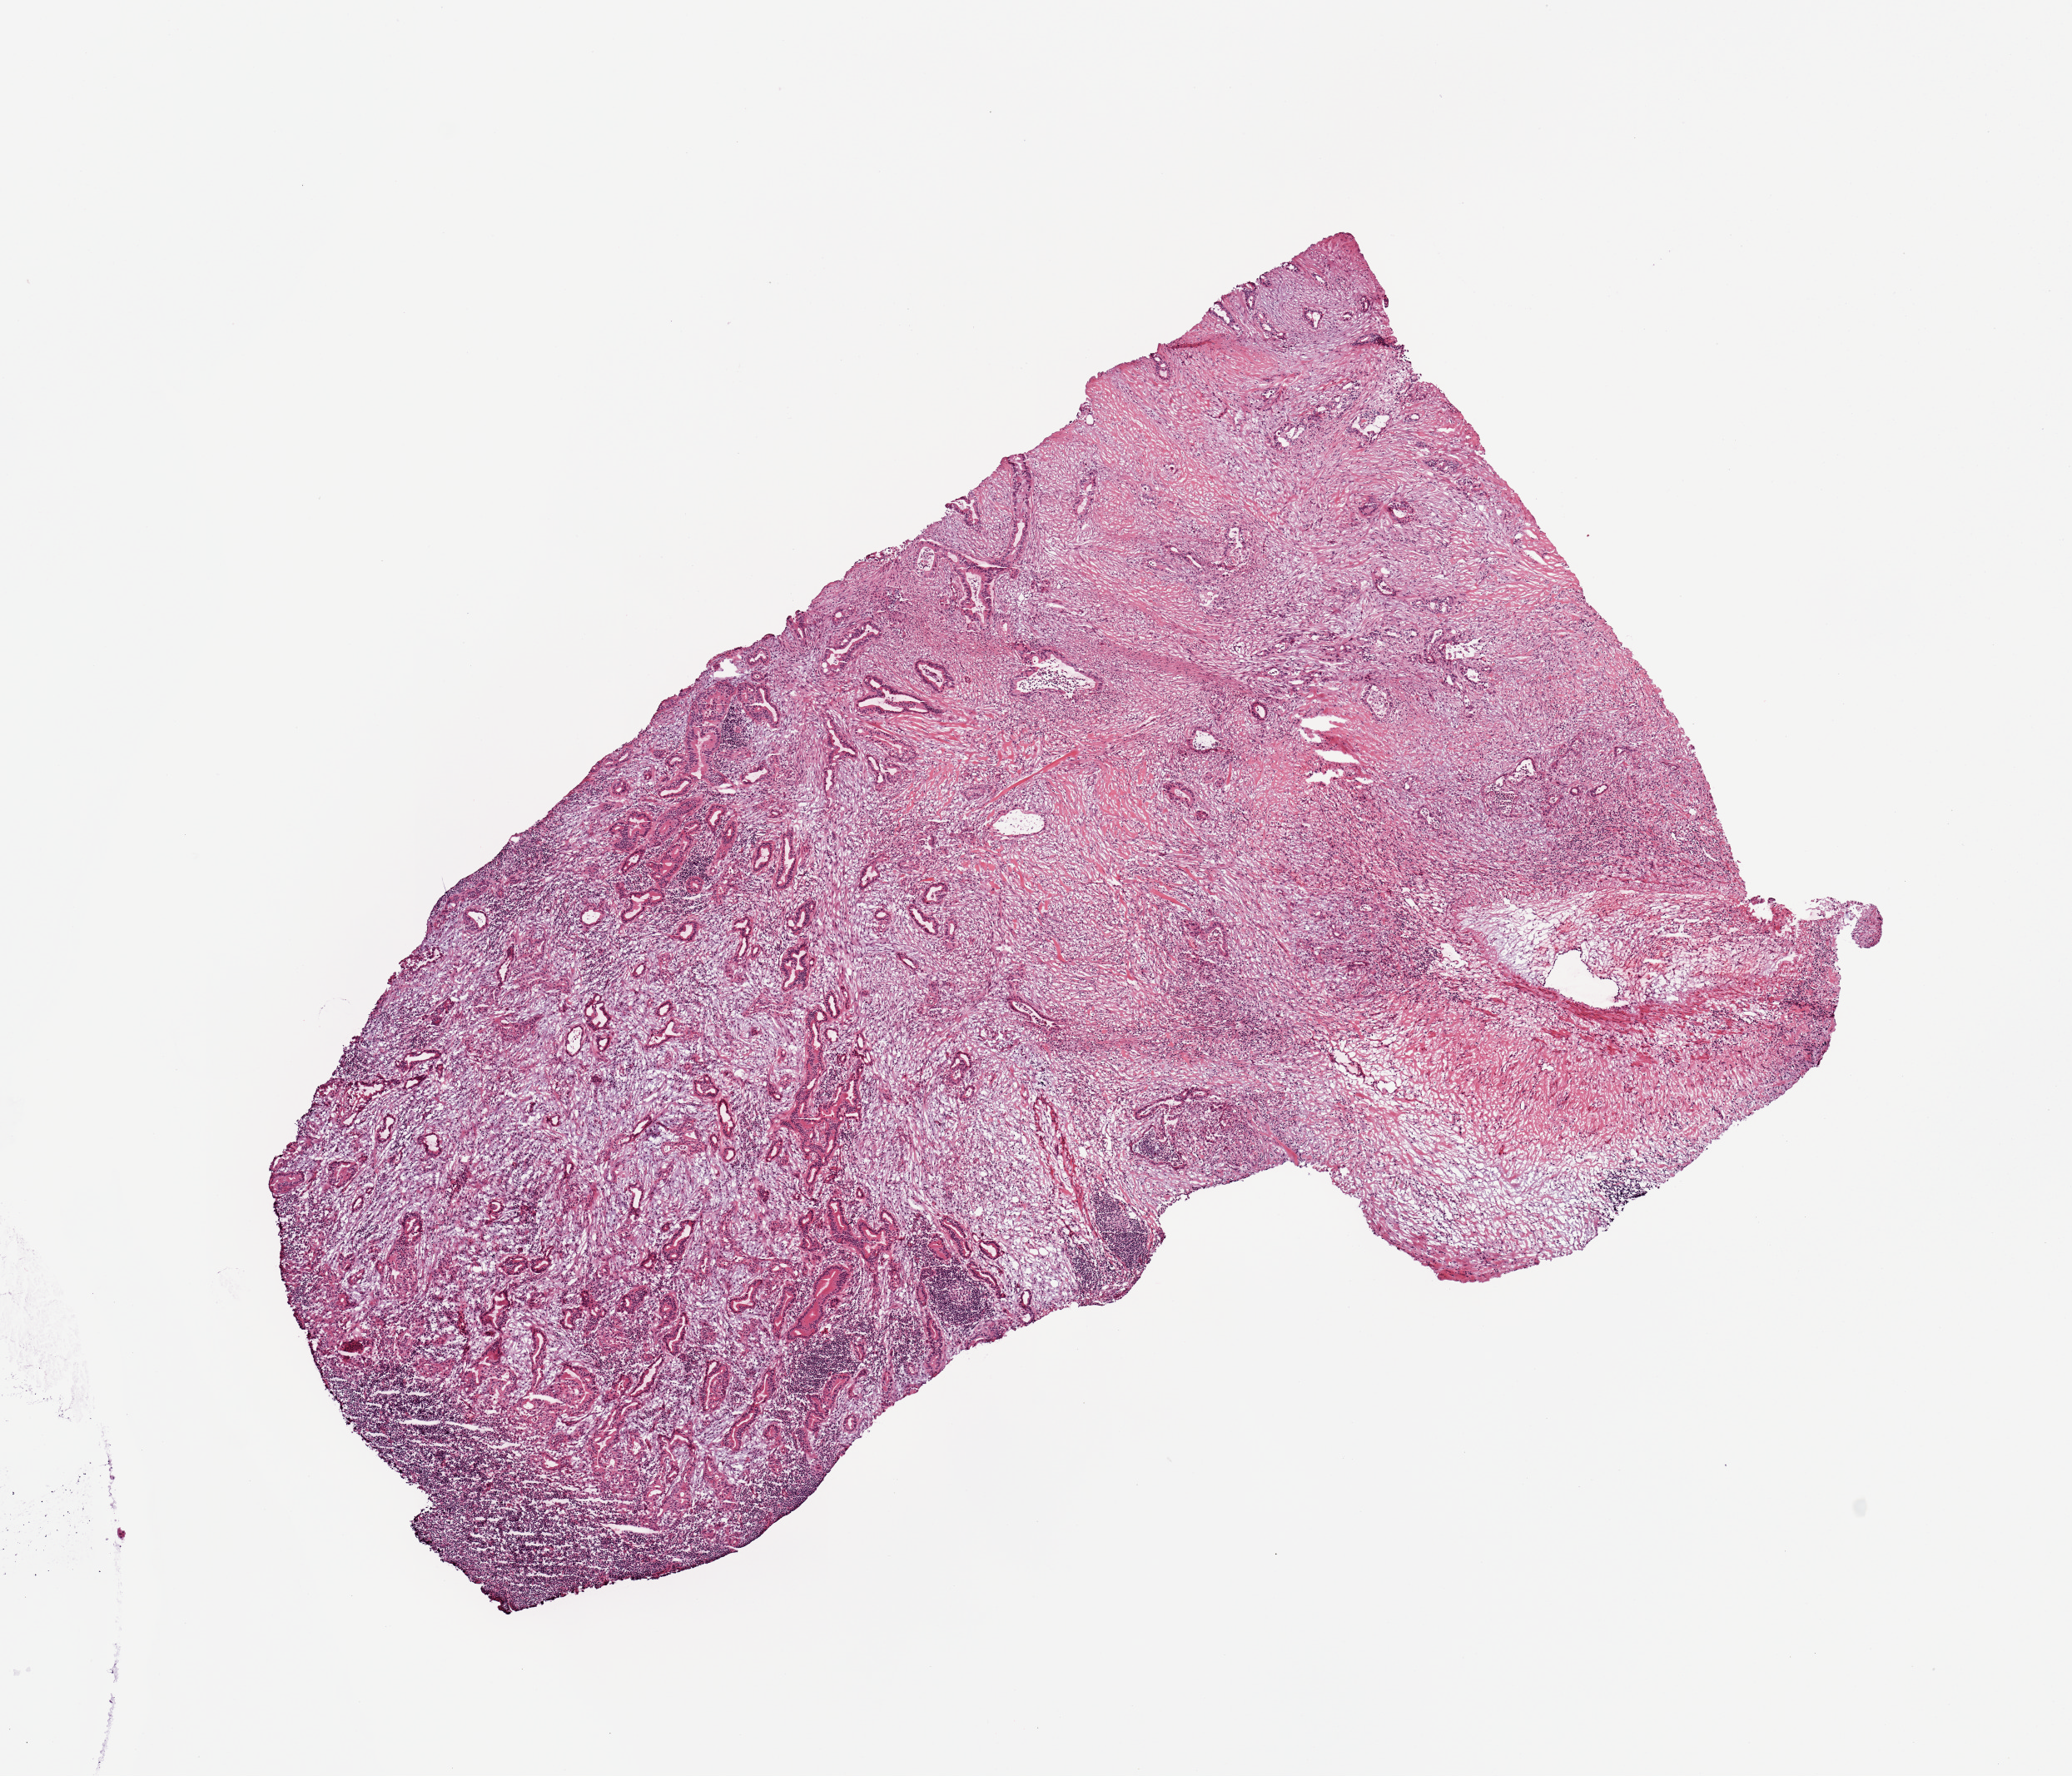
Digitized H&E-stained tissue section (whole slide), shown as a low-resolution overview of the whole scanned area (about 9.8 x 8.4 mm, slide scanned at 20x); tumour tissue sample, sampled site: pancreas. 59-year-old female patient. Histologic grade: G2 (moderately differentiated). Pathologist review of this section (percent, as recorded): tumour nuclei 30%, necrosis 0%.
- diagnosis: Infiltrating duct carcinoma, NOS
- AJCC pathologic stage: IIB
- primary tumour site (as recorded): body